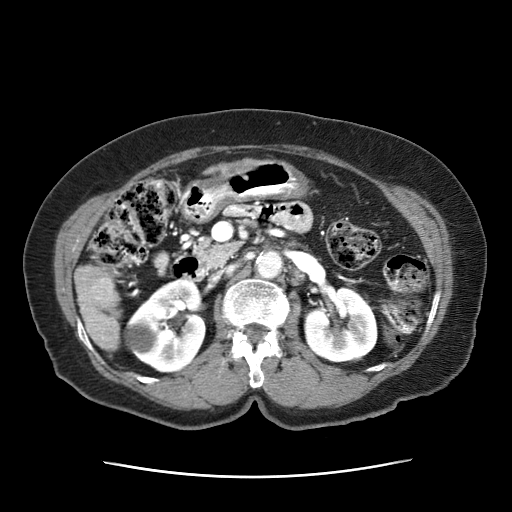
Contrast-enhanced abdominal CT (liver protocol), one axial slice; reconstruction kernel STANDARD; 120 kVp; soft-tissue window (W 400 / L 40 HU); 2.5 mm slice thickness; 512 × 512 image matrix, field of view 360 × 360 mm. Patient: female, 79 years. From the clinical record (not read from this slice): diagnosis: hepatocellular carcinoma (patient treated with transarterial chemoembolisation; whether this scan precedes or follows treatment is not stated here); TNM stage (as recorded): Stage-II; Child-Pugh class: B; tumour nodularity: multinodular.
Annotated regions visible in this slice (semi-automatic segmentation, software-assisted and operator-edited):
- abdominal aorta: box from (x=256, y=249) to (x=284, y=277) px
- liver parenchyma outside the tumour (the mass and vessels are separate outlines, so this box may not span the whole liver): (x=74, y=264)–(x=123, y=350)